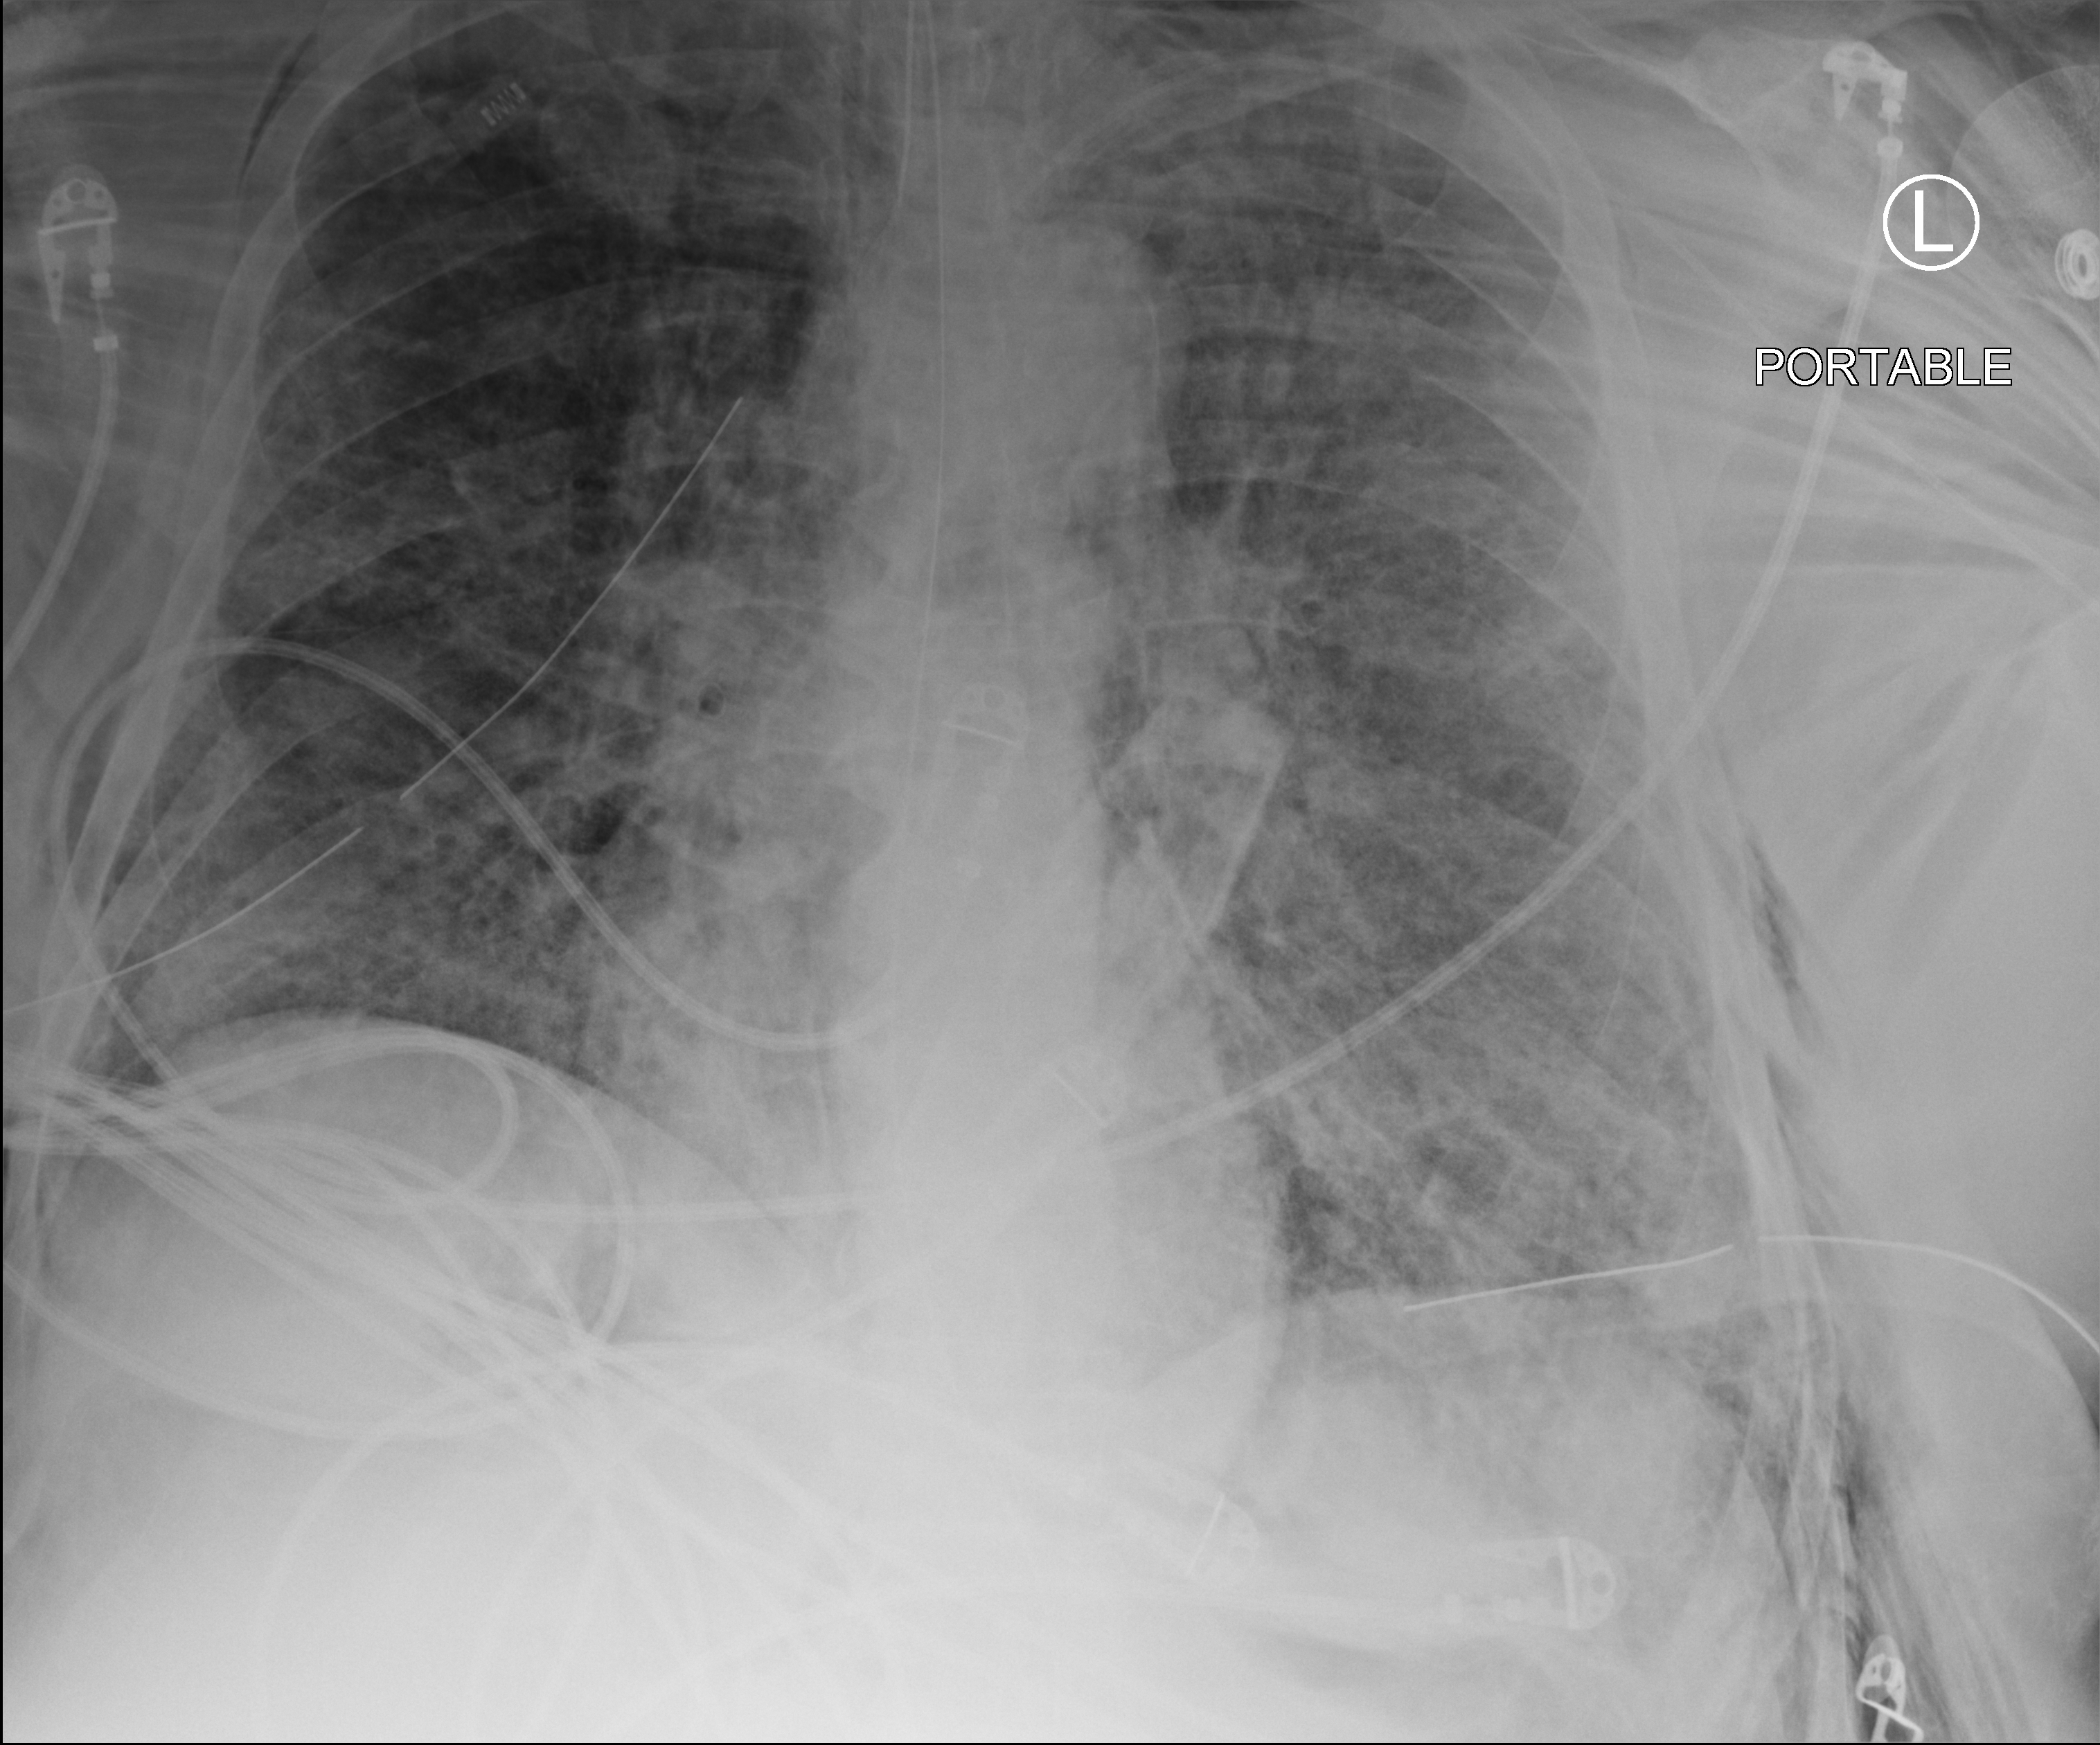
Chest X-ray (portable), anteroposterior (AP) projection. Patient hospitalised with COVID-19, aged 18–59 years.
Hospital-stay facts (about this admission, not read from this image; timing relative to this image not recorded): mechanically ventilated during this hospital stay: yes; hypertension (admission record): yes.